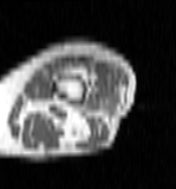
MRI of an extremity soft-tissue mass, one axial slice; slice 22 of 100 in the series (ordered by position); MR volume resampled by the dataset authors to the PET/CT grid (not the native acquisition matrix); 3.27 mm slice thickness; 176 × 189 image matrix, field of view 172 × 185 mm. Female patient. From the clinical record (not read from this slice): histological type: undifferentiated – high grade; grade: high; site of the primary tumour: left thigh.
Structures marked on this image (expert contour drawn on MRI and transferred to this co-registered scan by the dataset authors):
- gross tumour volume including surrounding oedema: box from (x=98, y=87) to (x=109, y=97) px